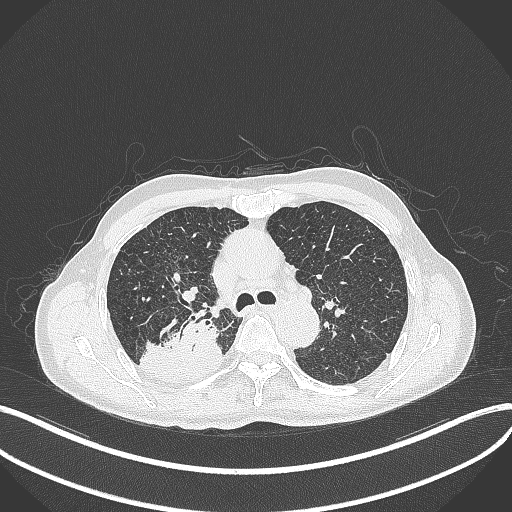
Chest CT, one axial slice; position 305 of 428 along the scan axis; reconstruction kernel B70f; 120 kVp; lung window (W 1500 / L -600 HU); 512 × 512 image matrix, field of view 400 × 400 mm. Patient: male, 79 years. From the clinical record (not read from this slice): clinical TNM (as recorded): T3 N0 M0.
Outlined on this slice (rectangle marked by the reading radiologist):
- lung tumour (recorded histology: adenocarcinoma): bounding box (x1, y1, x2, y2) in pixels: (139, 309, 224, 384)